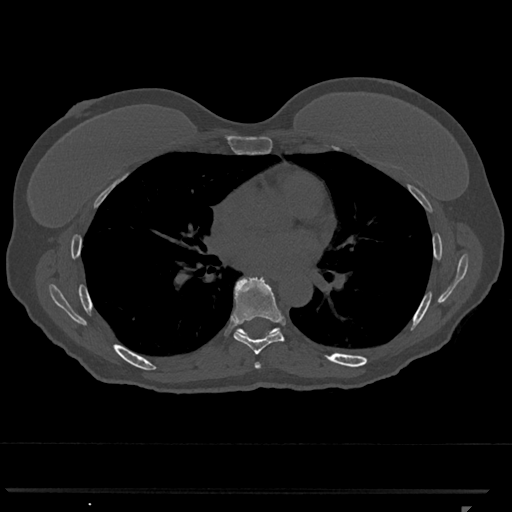
CT including the spine, one axial slice; position 704 of 793 along the scan axis; reconstruction kernel Br40s/3; 120 kVp; bone window (W 1800 / L 400 HU); 0.5 mm slice thickness; 512 × 512 image matrix, field of view 380 × 380 mm. Female patient, age 62 years. From the clinical record (not read from this slice): primary cancer: renal.
Structures marked on this image (semi-automatic segmentation, software-assisted and operator-edited):
- T6 vertebra: bounding box [x1, y1, x2, y2] px = [254, 362, 261, 369]
- T7 vertebra: [232, 277, 294, 354]
- T8 vertebra: [239, 328, 276, 333]